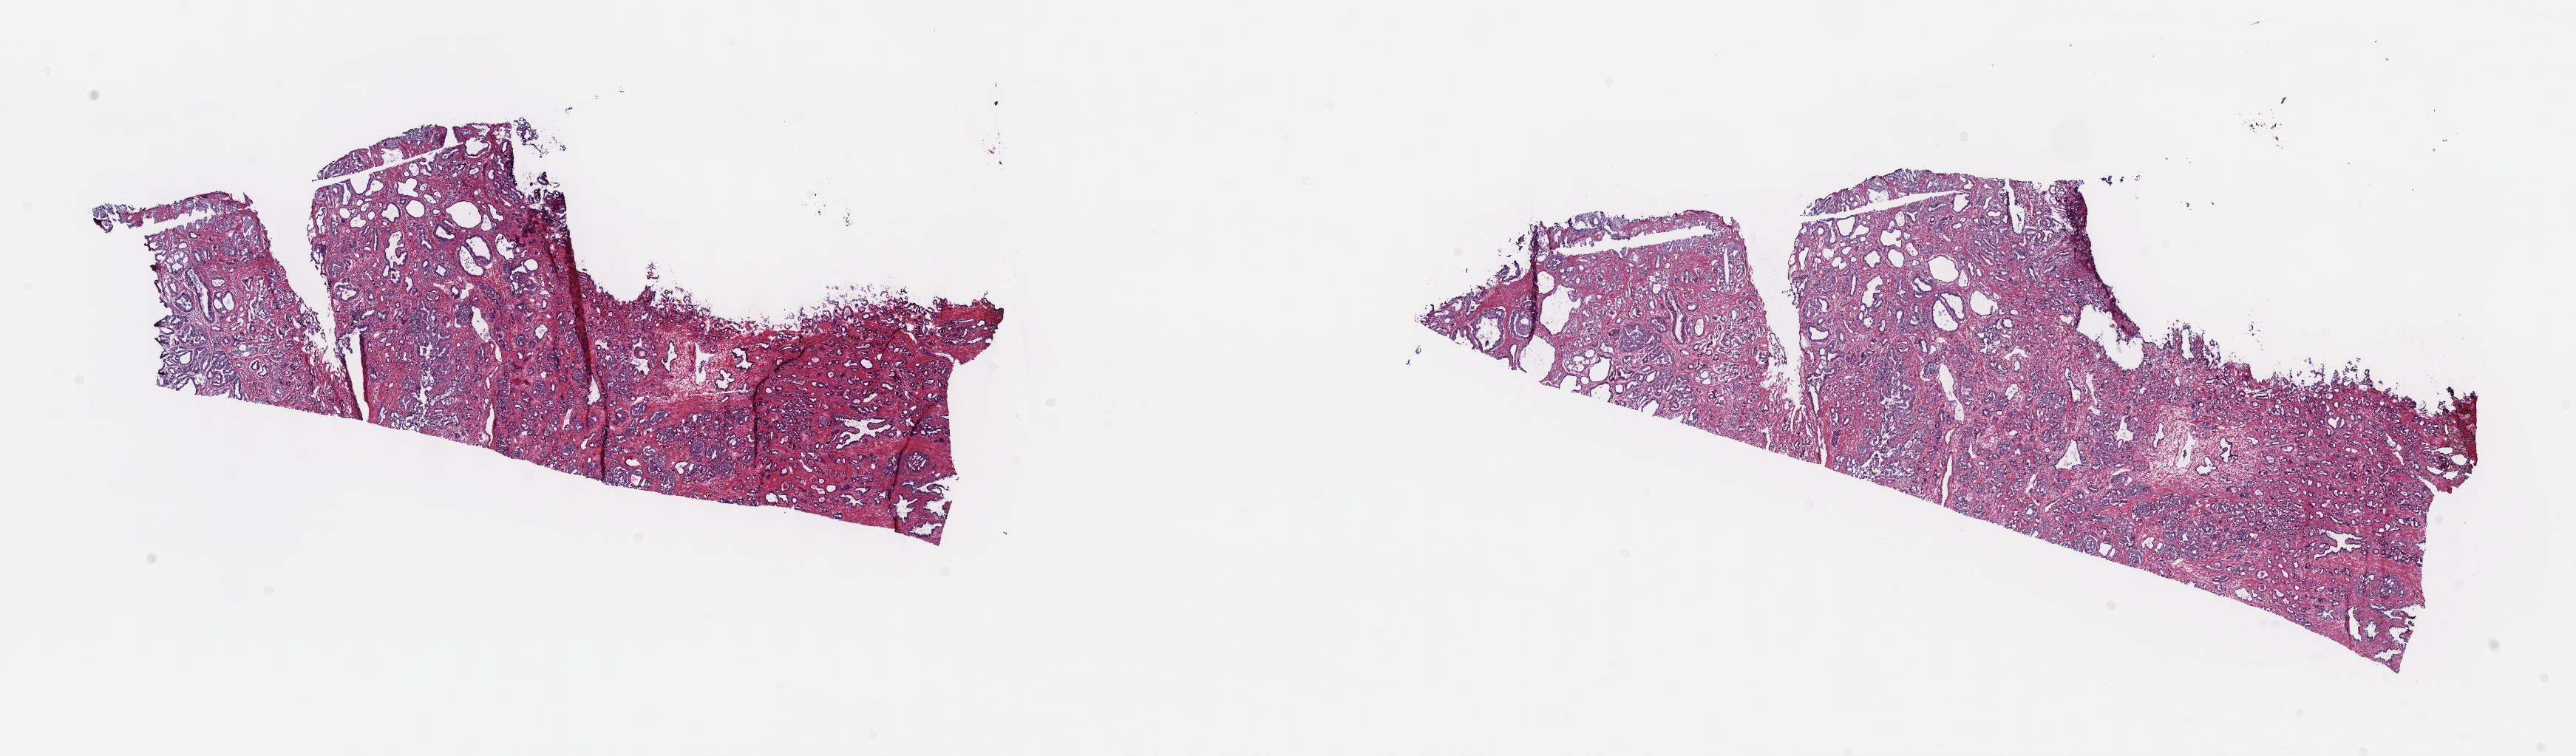
Whole-slide histology image, H&E, a low-resolution overview of the entire scanned area, about 28.2 x 8.3 mm; frozen section from the top of the tissue portion; sample: primary tumour, prostate. Patient: male, age at initial diagnosis 58 years. Gleason score: 7 (4+3). Slide review estimates, as recorded: tumour cells 100%, tumour nuclei 70%, normal cells 0%, stromal cells 0%, necrosis 0%. Infiltration values recorded for this section: lymphocyte infiltration 2%, monocyte infiltration 0%, neutrophil infiltration 0%.
Laterality: bilateral. Histologic diagnosis: Adenocarcinoma, NOS (prostate gland). Lymph nodes positive (case pathology): 0 of 23 examined.